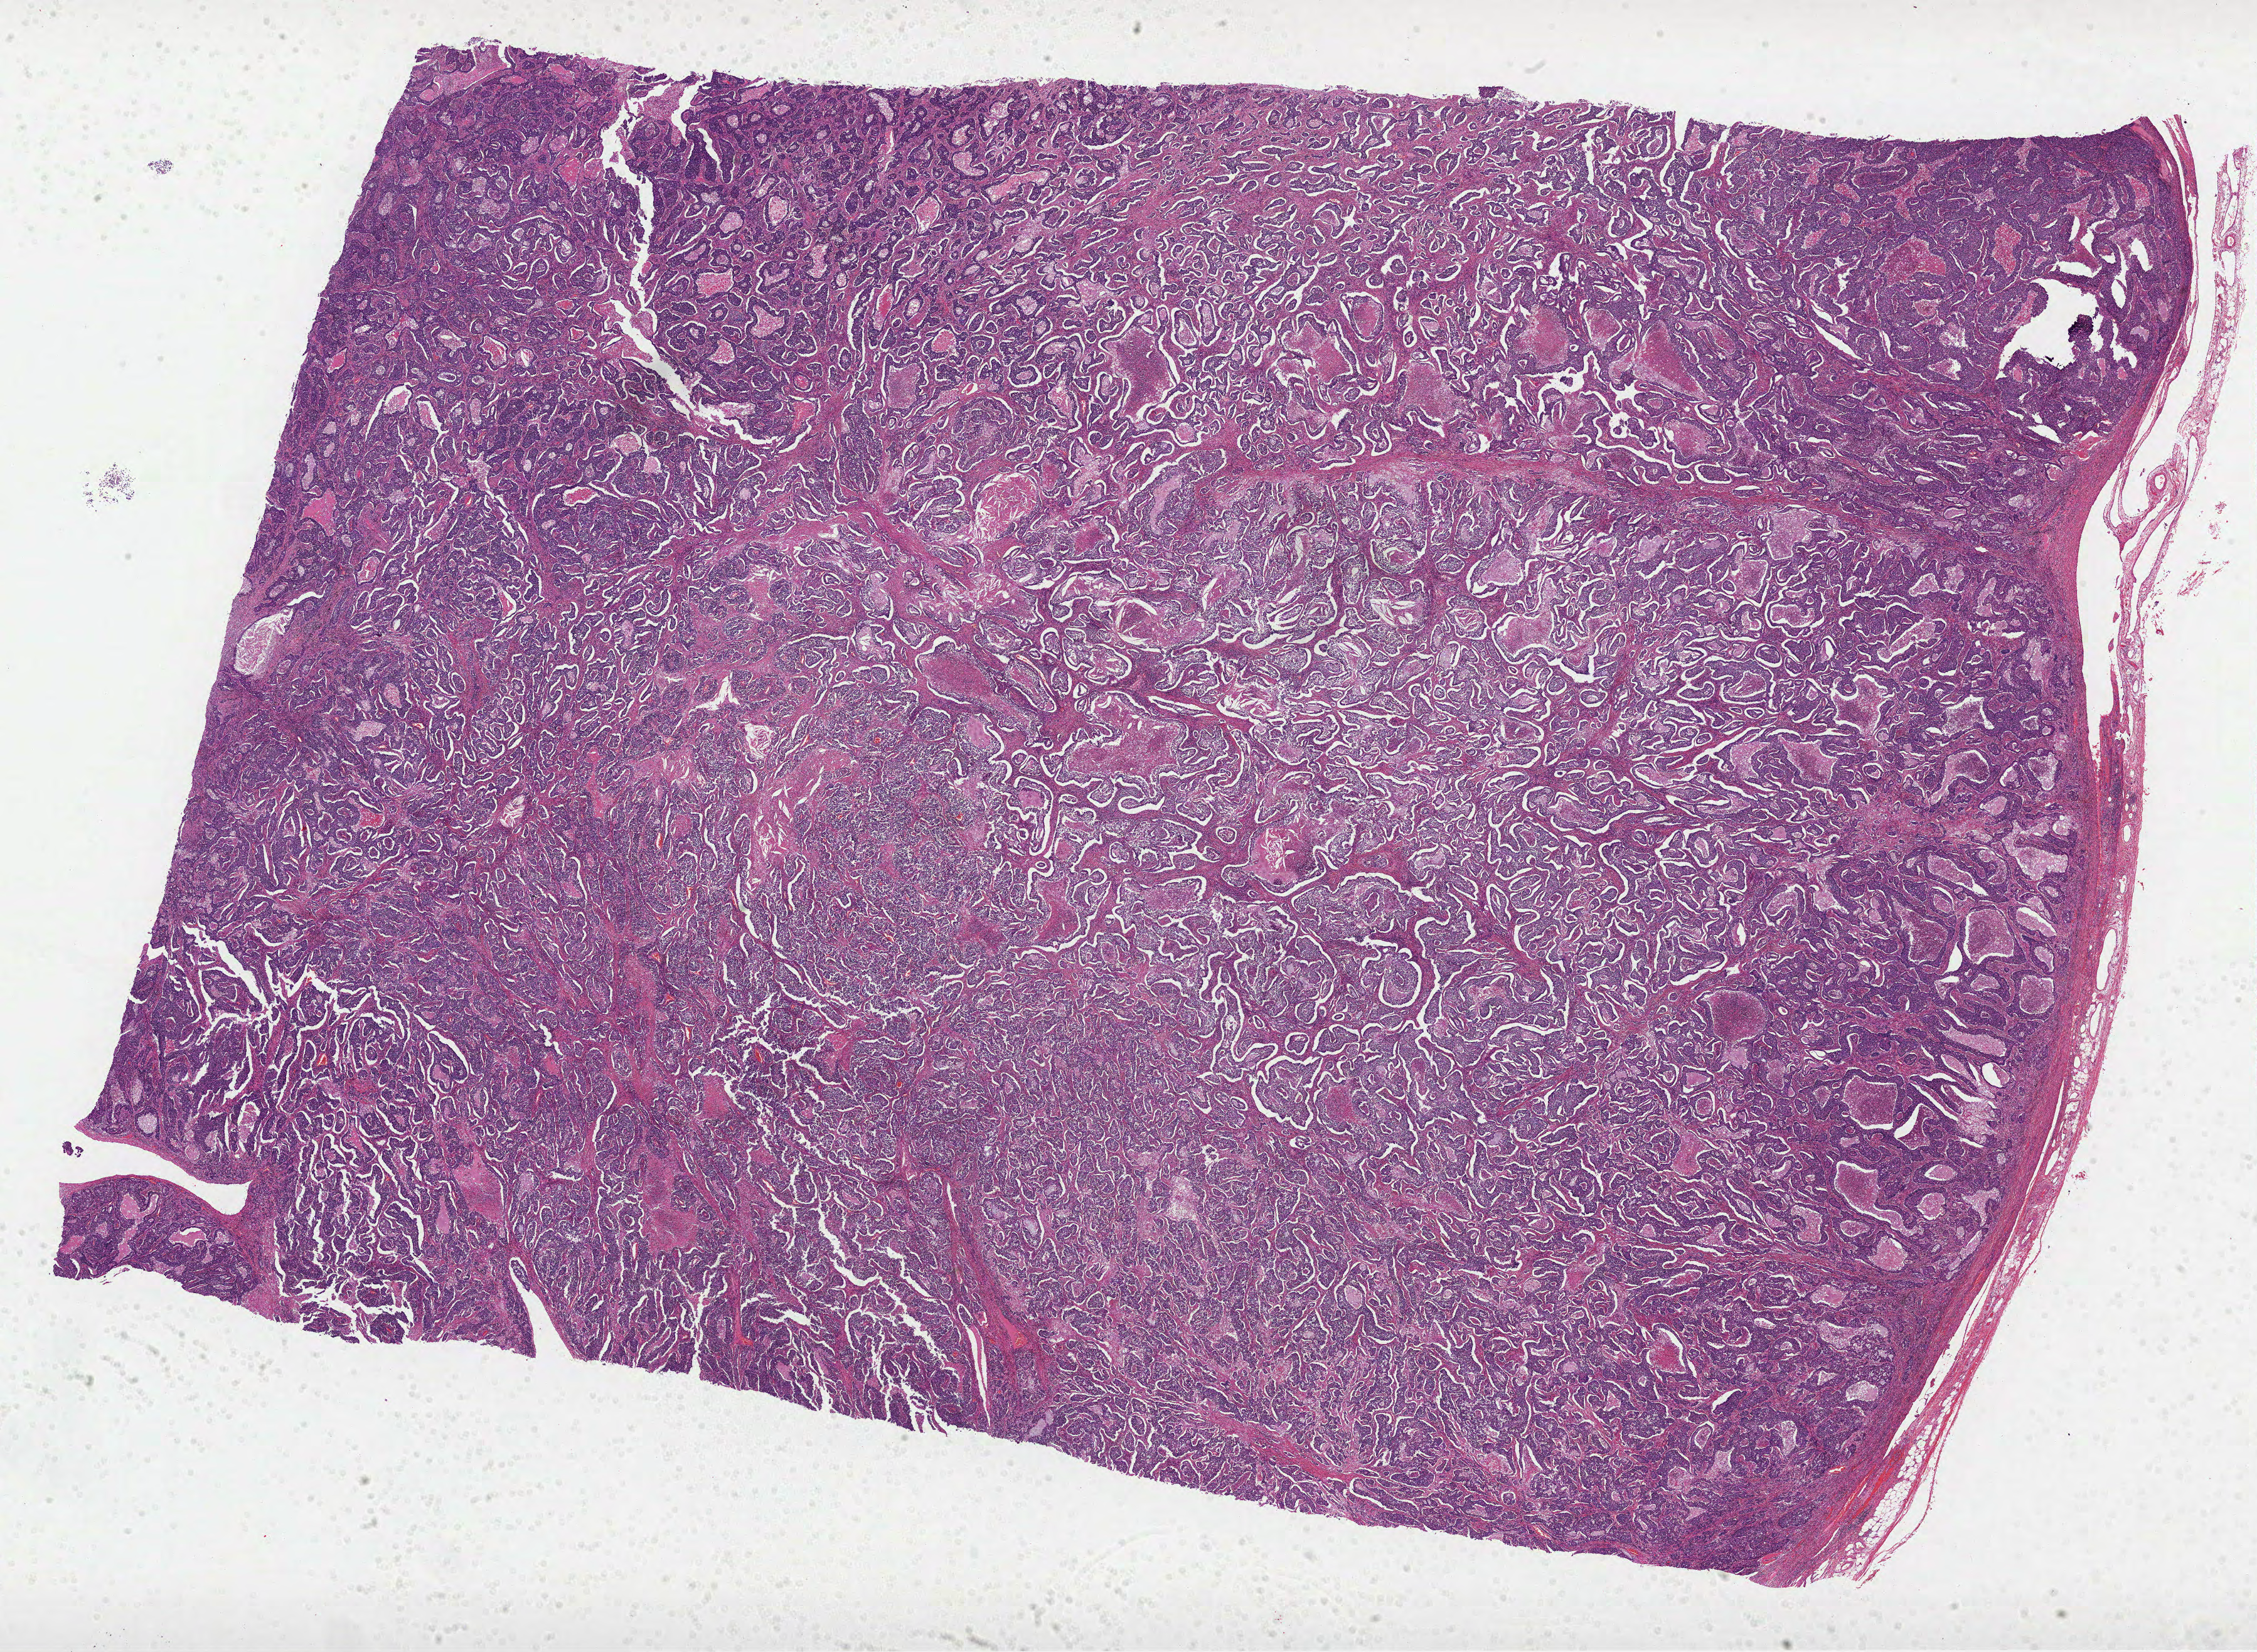
Digitized Hematoxylin and eosin (H&E) stained tissue section (whole slide) — whole scanned area (about 29.0 x 21.2 mm) shown as a low-resolution overview; formalin-fixed paraffin-embedded (FFPE) diagnostic section; primary tumour sample from the lung. Patient: male, age at initial diagnosis 69 years.
Diagnosis: Adenocarcinoma, NOS (upper lobe, lung).